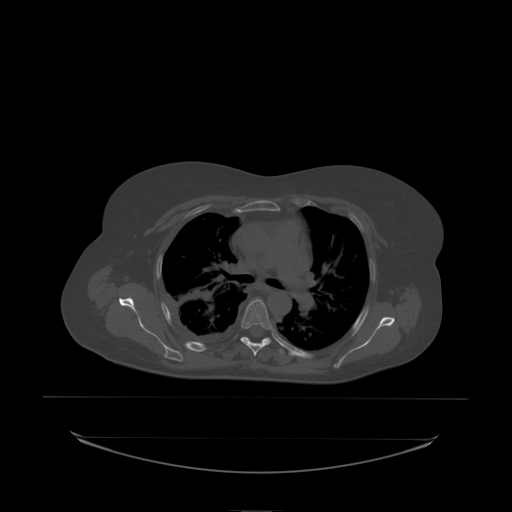
CT including the spine, one axial slice; slice 157 of 242 in the series (ordered by position); bone window (W 1800 / L 400 HU); 512 × 512 image matrix, field of view 500 × 500 mm. Female patient, age 53 years. Case-level facts recorded for this patient, not image findings: primary cancer: lung.
Annotated regions visible in this slice (semi-automatic segmentation, software-assisted and operator-edited):
- T5 vertebra: box from (x=241, y=300) to (x=273, y=330) px
- T6 vertebra: (x=245, y=328)–(x=274, y=338)